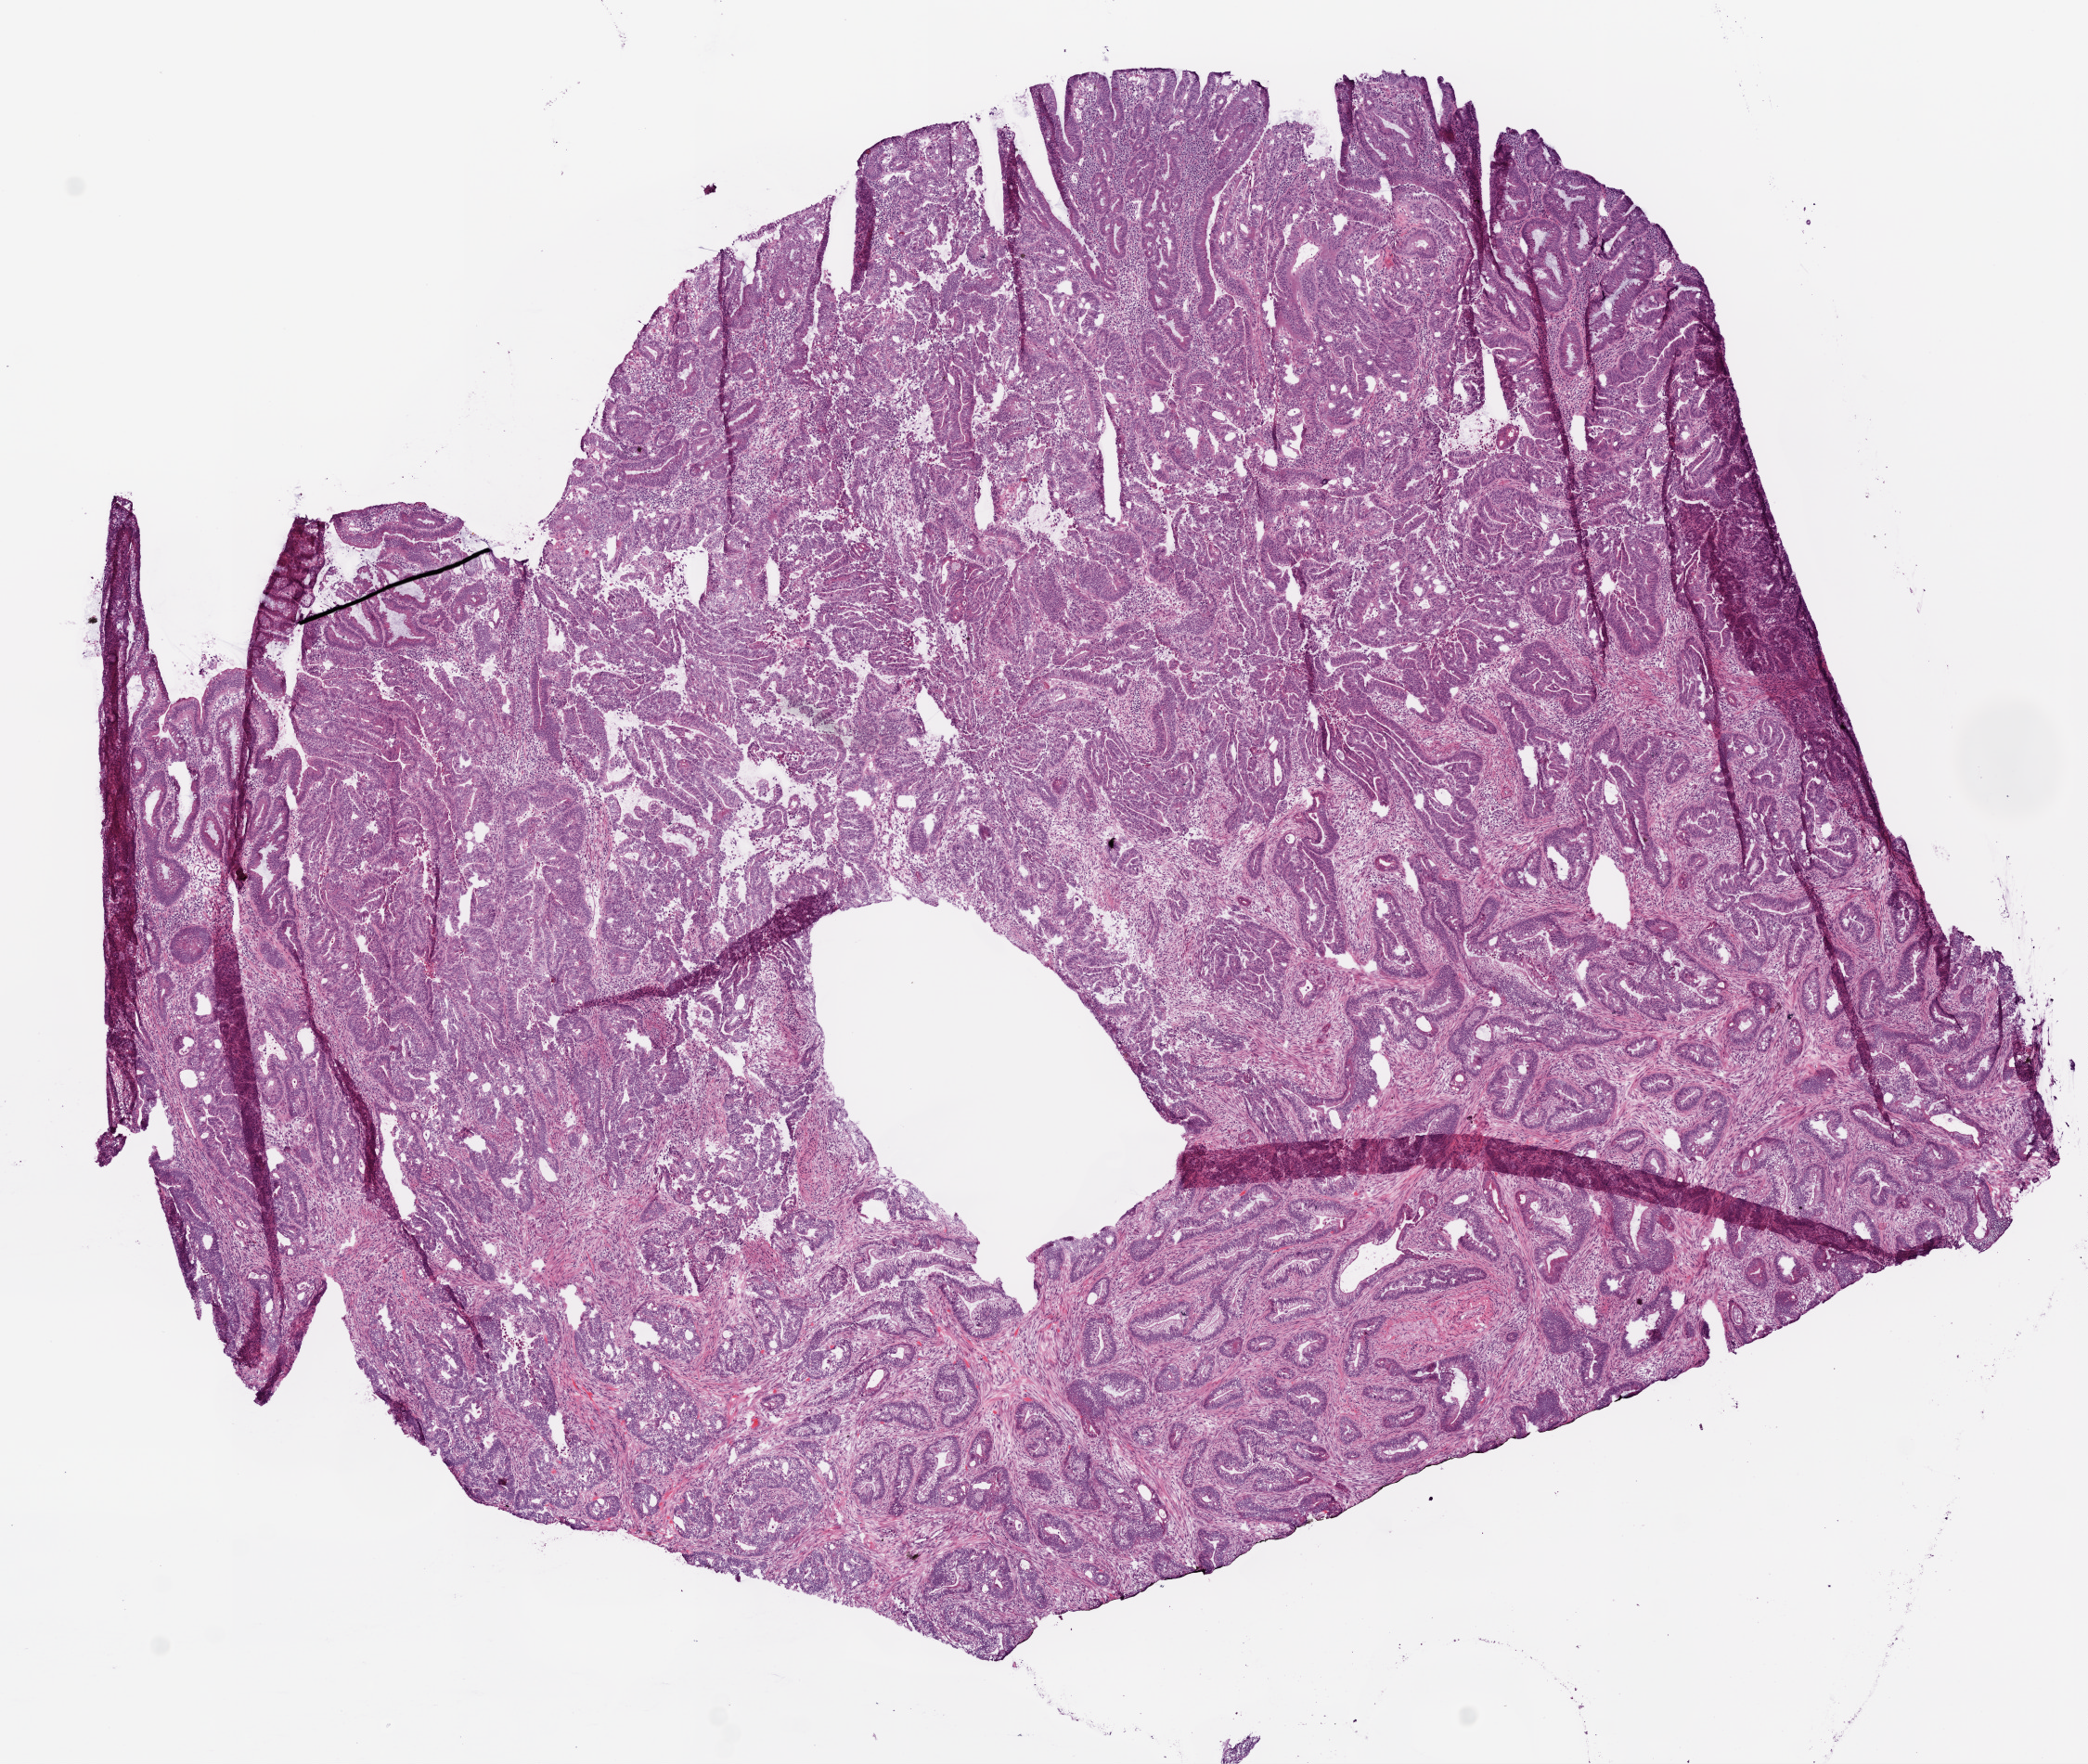
Digitized H&E-stained tissue section (whole slide) — shown as a low-resolution overview of the whole scanned area (about 9.0 x 7.6 mm, from a 20x scan). Frozen section. Primary tumour sample from the colon. Patient: female, age at initial diagnosis 57 years. Composition of this section per pathologist review: tumour cells 70%, tumour nuclei 75%, normal cells 15%, stromal cells 10%, necrosis 5%.
Lymph nodes positive (case pathology): 2 of 28 examined. AJCC pathologic stage: IIIB (7th edition). Histologic diagnosis: Adenocarcinoma, NOS. TNM: T3 N1b M0.